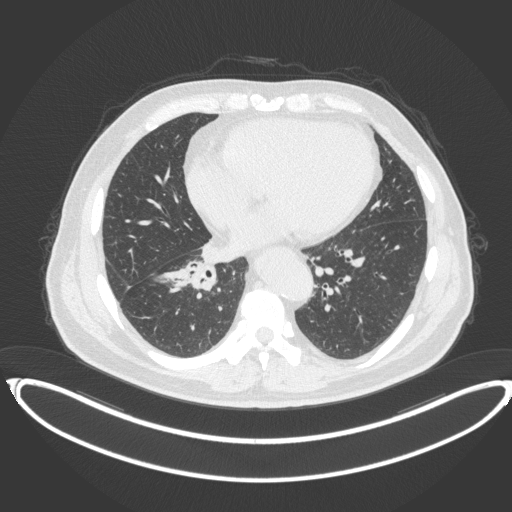
Chest CT, one axial slice; slice 163 of 383 in the series (ordered by position); lung window (W 1500 / L -600 HU); 1 mm slice thickness; 512 × 512 image matrix, field of view 448 × 448 mm. Male patient, age 61 years. From the clinical record (not read from this slice): clinical TNM (as recorded): T1b N1 M0.
Outlined on this slice (bounding box drawn by a radiologist):
- lung tumour (recorded histology: squamous cell carcinoma): box from (x=183, y=260) to (x=216, y=292) px